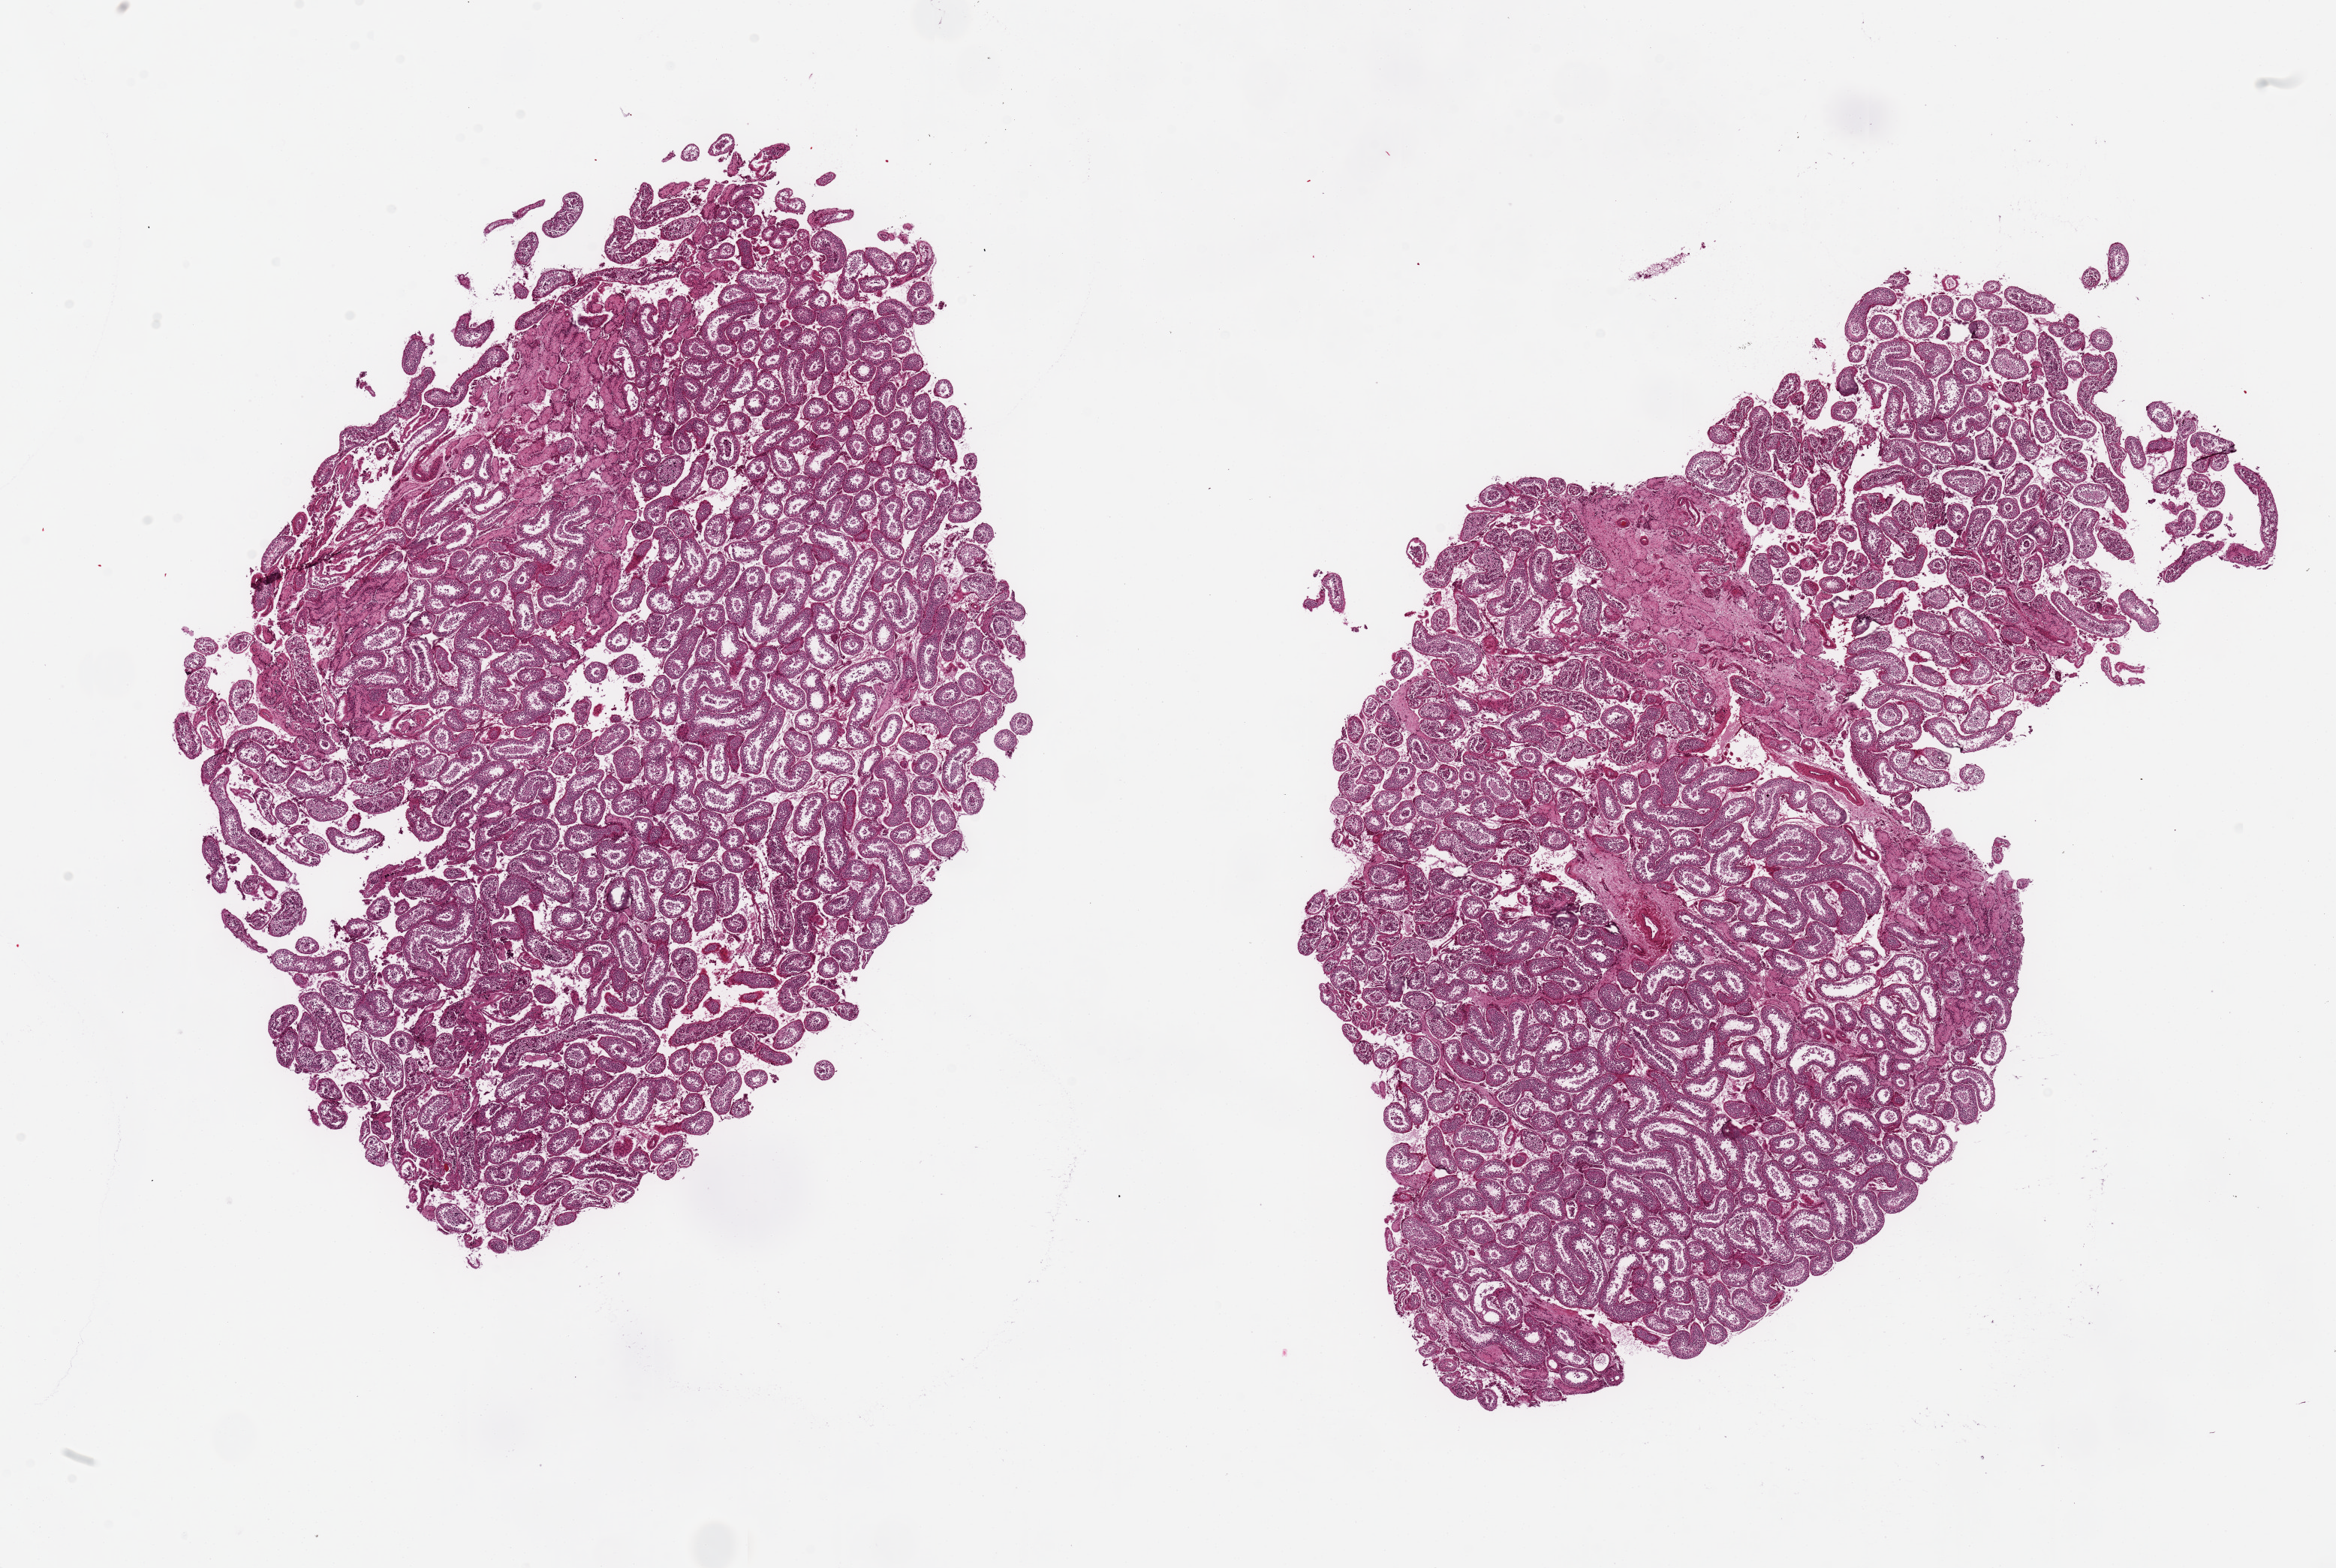
Digitized H&E-stained section — a low-resolution overview of the entire scanned area, about 24.6 x 16.5 mm (from a 20x scan). PAXgene-fixed, paraffin-embedded tissue. Sampled site (target tissue): testis. Tissue donor sample. Donor sex: male.
• pathologist's review note for this sample: 2 pieces, 11x9 & 13x9mm; adequate spermatogenesis; focal tubular atrophy/fibrosis up to 3x1mm c/w microinfarcts